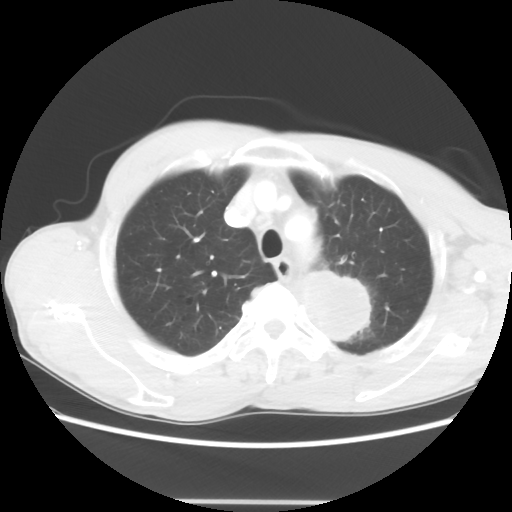
Chest CT, one axial slice; slice 52 of 62 in the series (ordered by position); lung window (W 1500 / L -600 HU); 512 × 512 image matrix. Male patient, age 61 years. From the clinical record (not read from this slice): clinical TNM (as recorded): T3 N1 M1.
Annotated regions visible in this slice (bounding box drawn by a radiologist):
- lung tumour (recorded histology: adenocarcinoma): bounding box (x1, y1, x2, y2) in pixels: (297, 267, 377, 352)